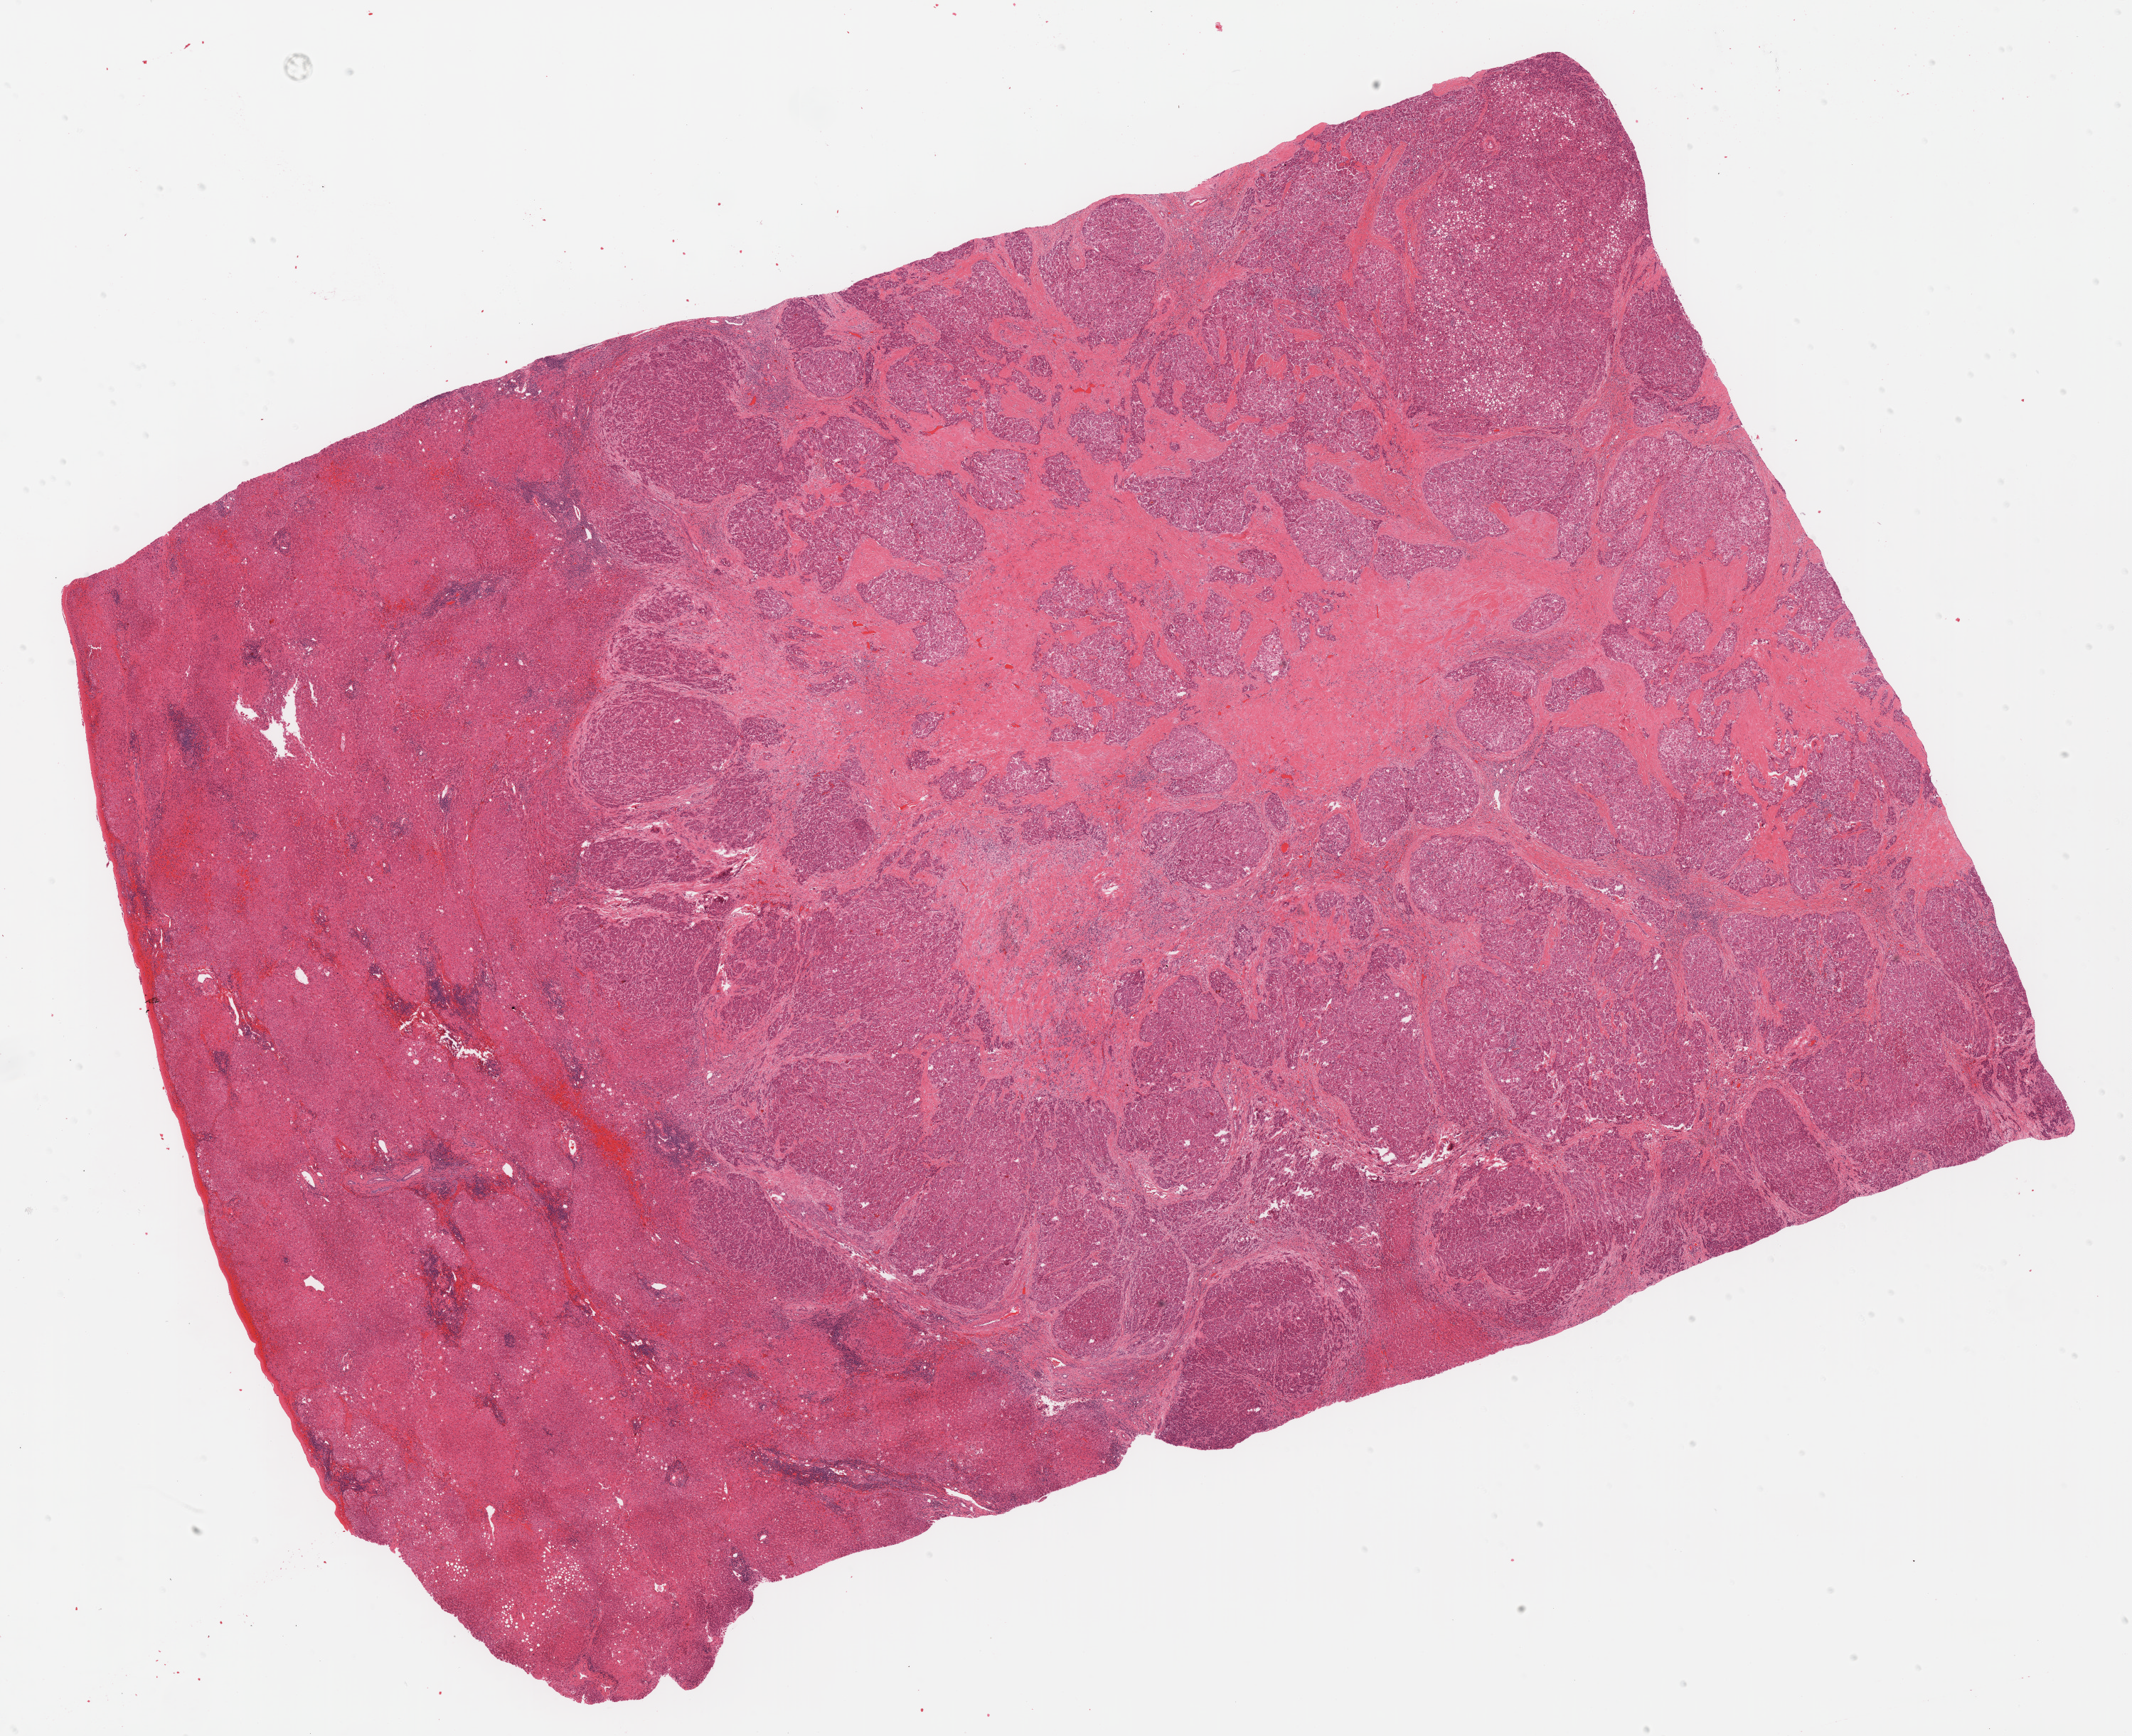
Whole-slide histology image, H&E-stained — shown as a low-resolution overview of the whole scanned area (about 24.0 x 19.5 mm, slide scanned at 20x); formalin-fixed paraffin-embedded (FFPE) diagnostic section; liver, primary tumour sample. Patient: male, age at initial diagnosis 62 years. Histologic grade: G2 (moderately differentiated).
* histologic diagnosis: Hepatocellular carcinoma, NOS
* AJCC pathologic stage: I (6th edition)
* TNM: T1 NX M0